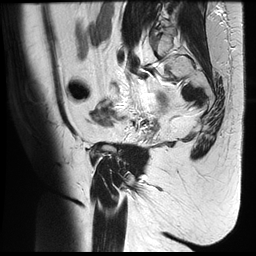
Pelvic MRI for cervical cancer, one sagittal slice; slice 9 of 35 in the series (ordered by position); T2-weighted; 1.5 T; TE 122.8 ms, TR 4992 ms; 4 mm slice thickness; 256 × 256 image matrix. Female patient, age 42 years.
Outlined on this slice (outlined manually by an expert reader):
- uterus and cervix: box from (x=89, y=107) to (x=115, y=128) px